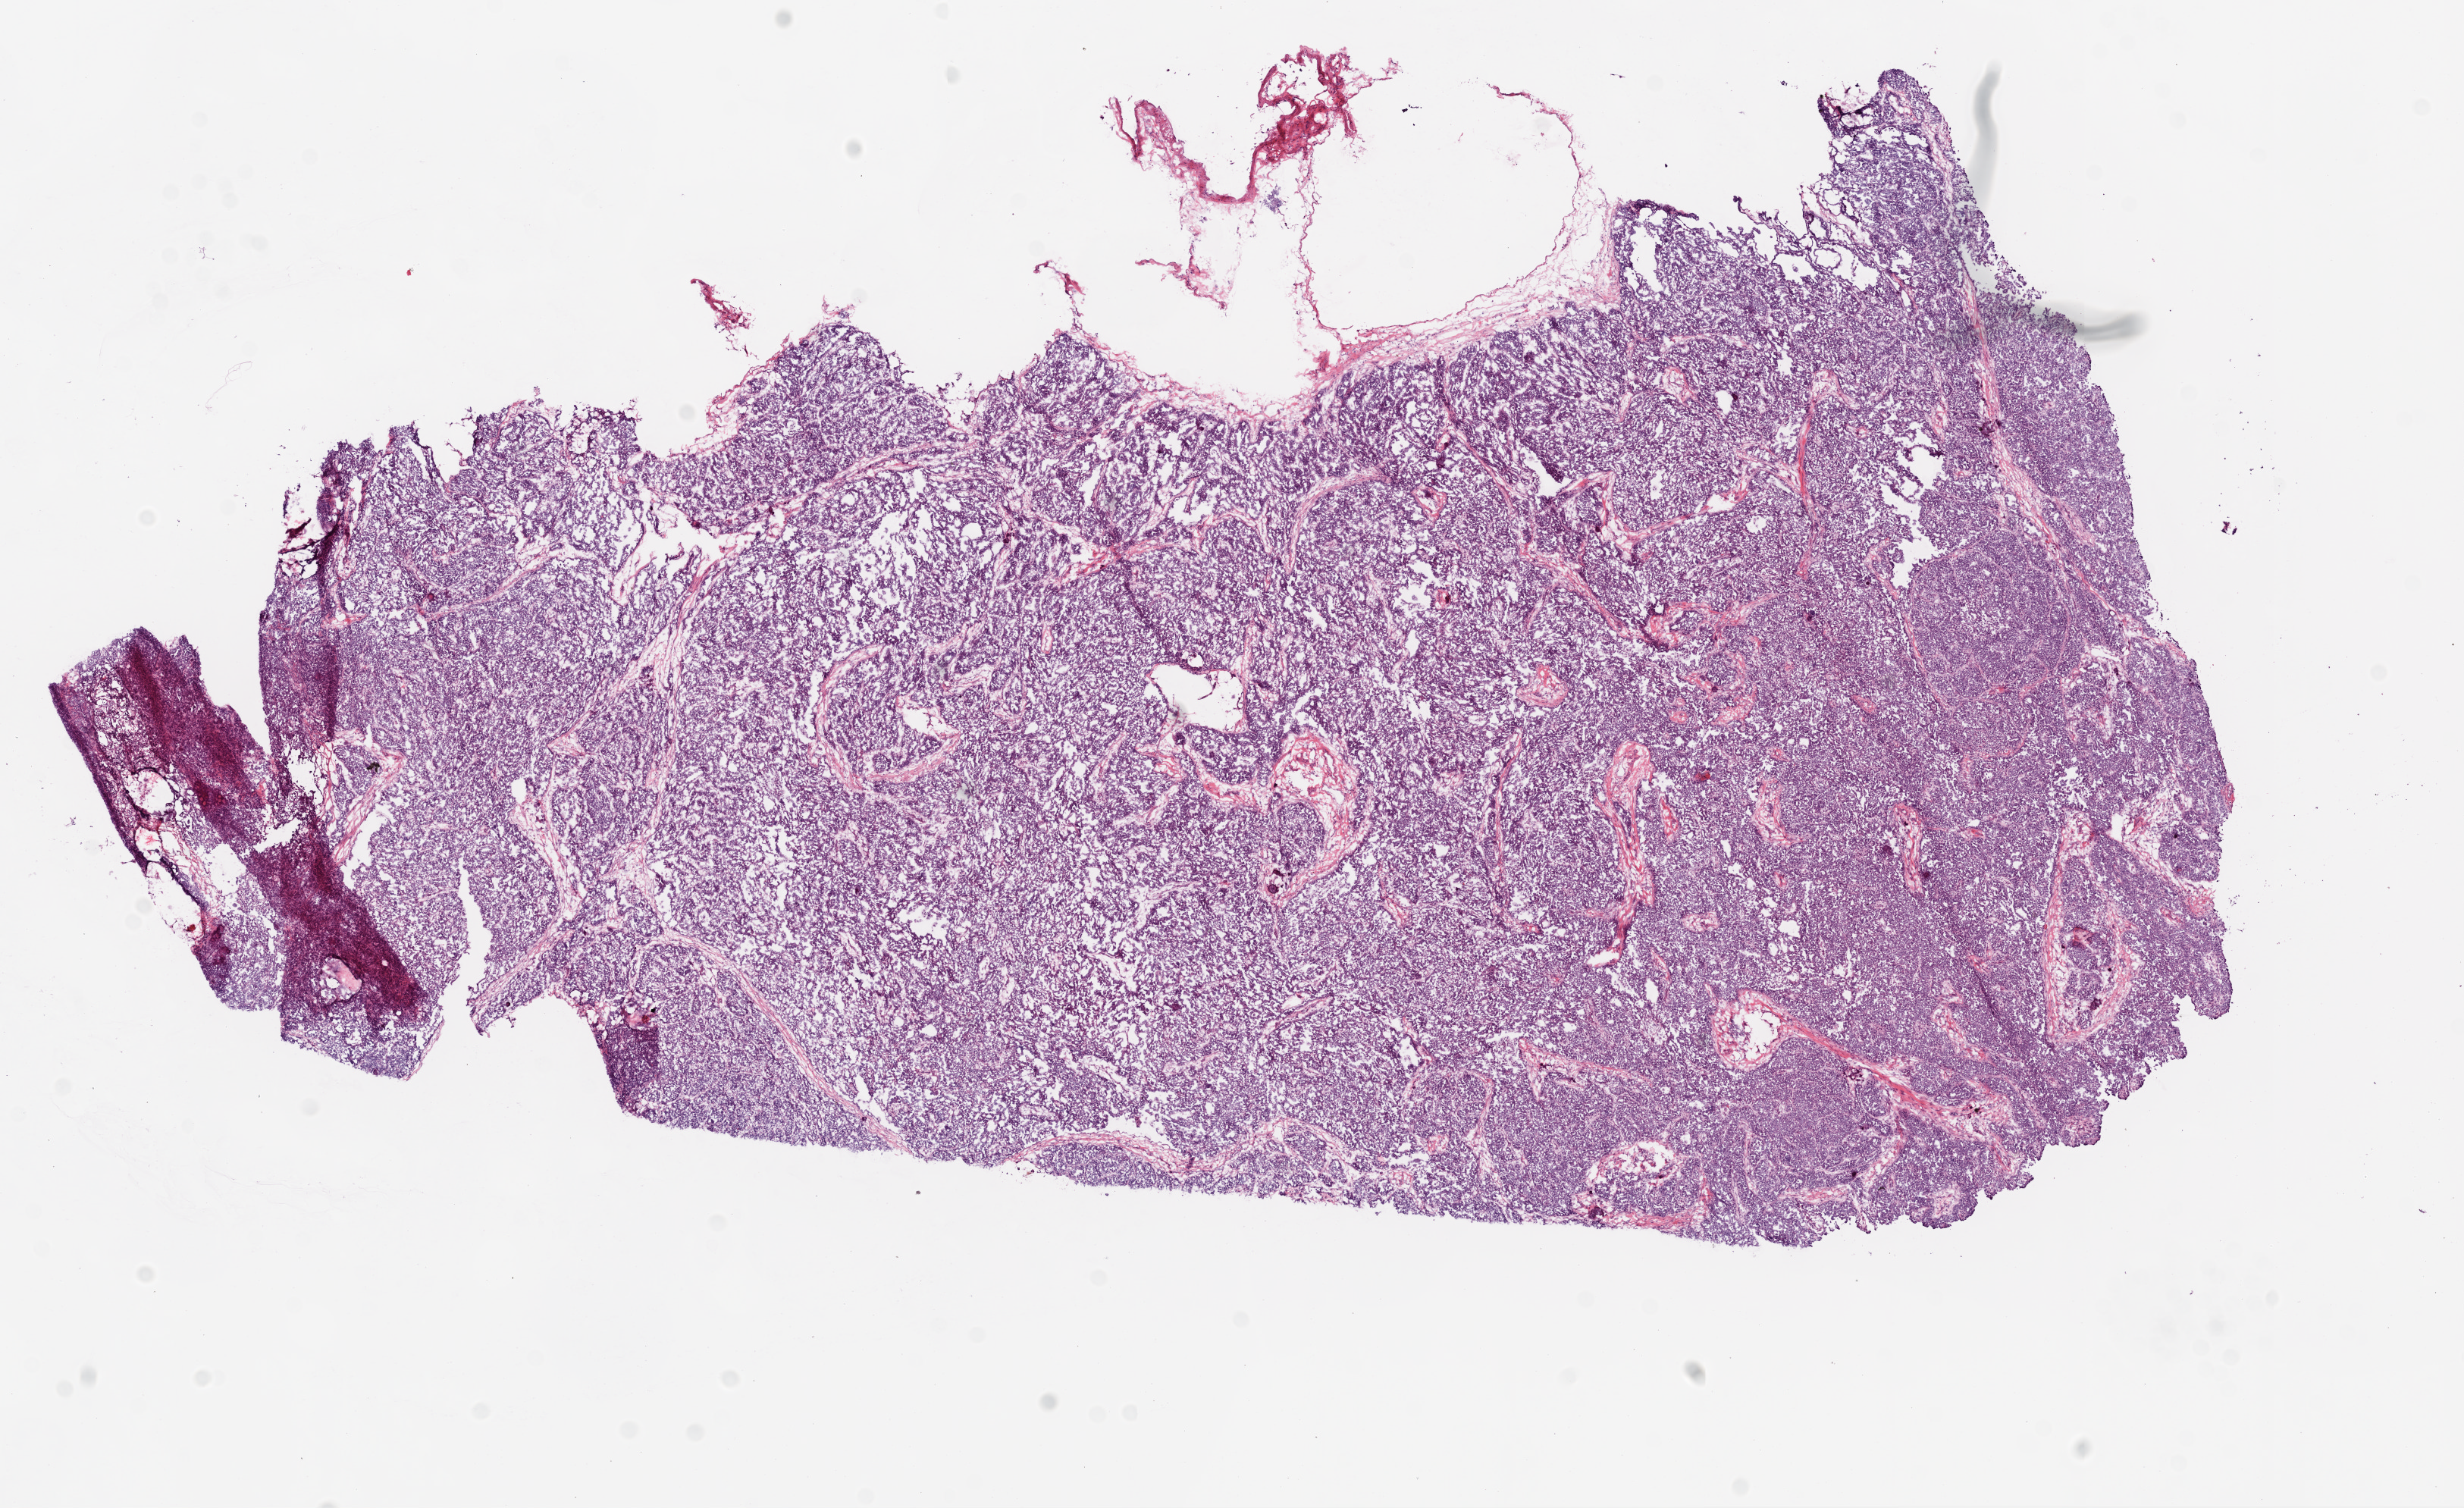
Whole-slide histology image, H&E, a low-resolution overview of the entire scanned area, about 13.0 x 8.0 mm (from a 20x scan), frozen section from the top of the tissue portion, ovary, primary tumour sample. Patient: female, age at initial diagnosis 80 years. Pathologist review of this section (percent, as recorded): tumour cells 95%, tumour nuclei 95%, normal cells 0%, stromal cells 5%, necrosis 0%.
• histologic diagnosis: Serous cystadenocarcinoma, NOS